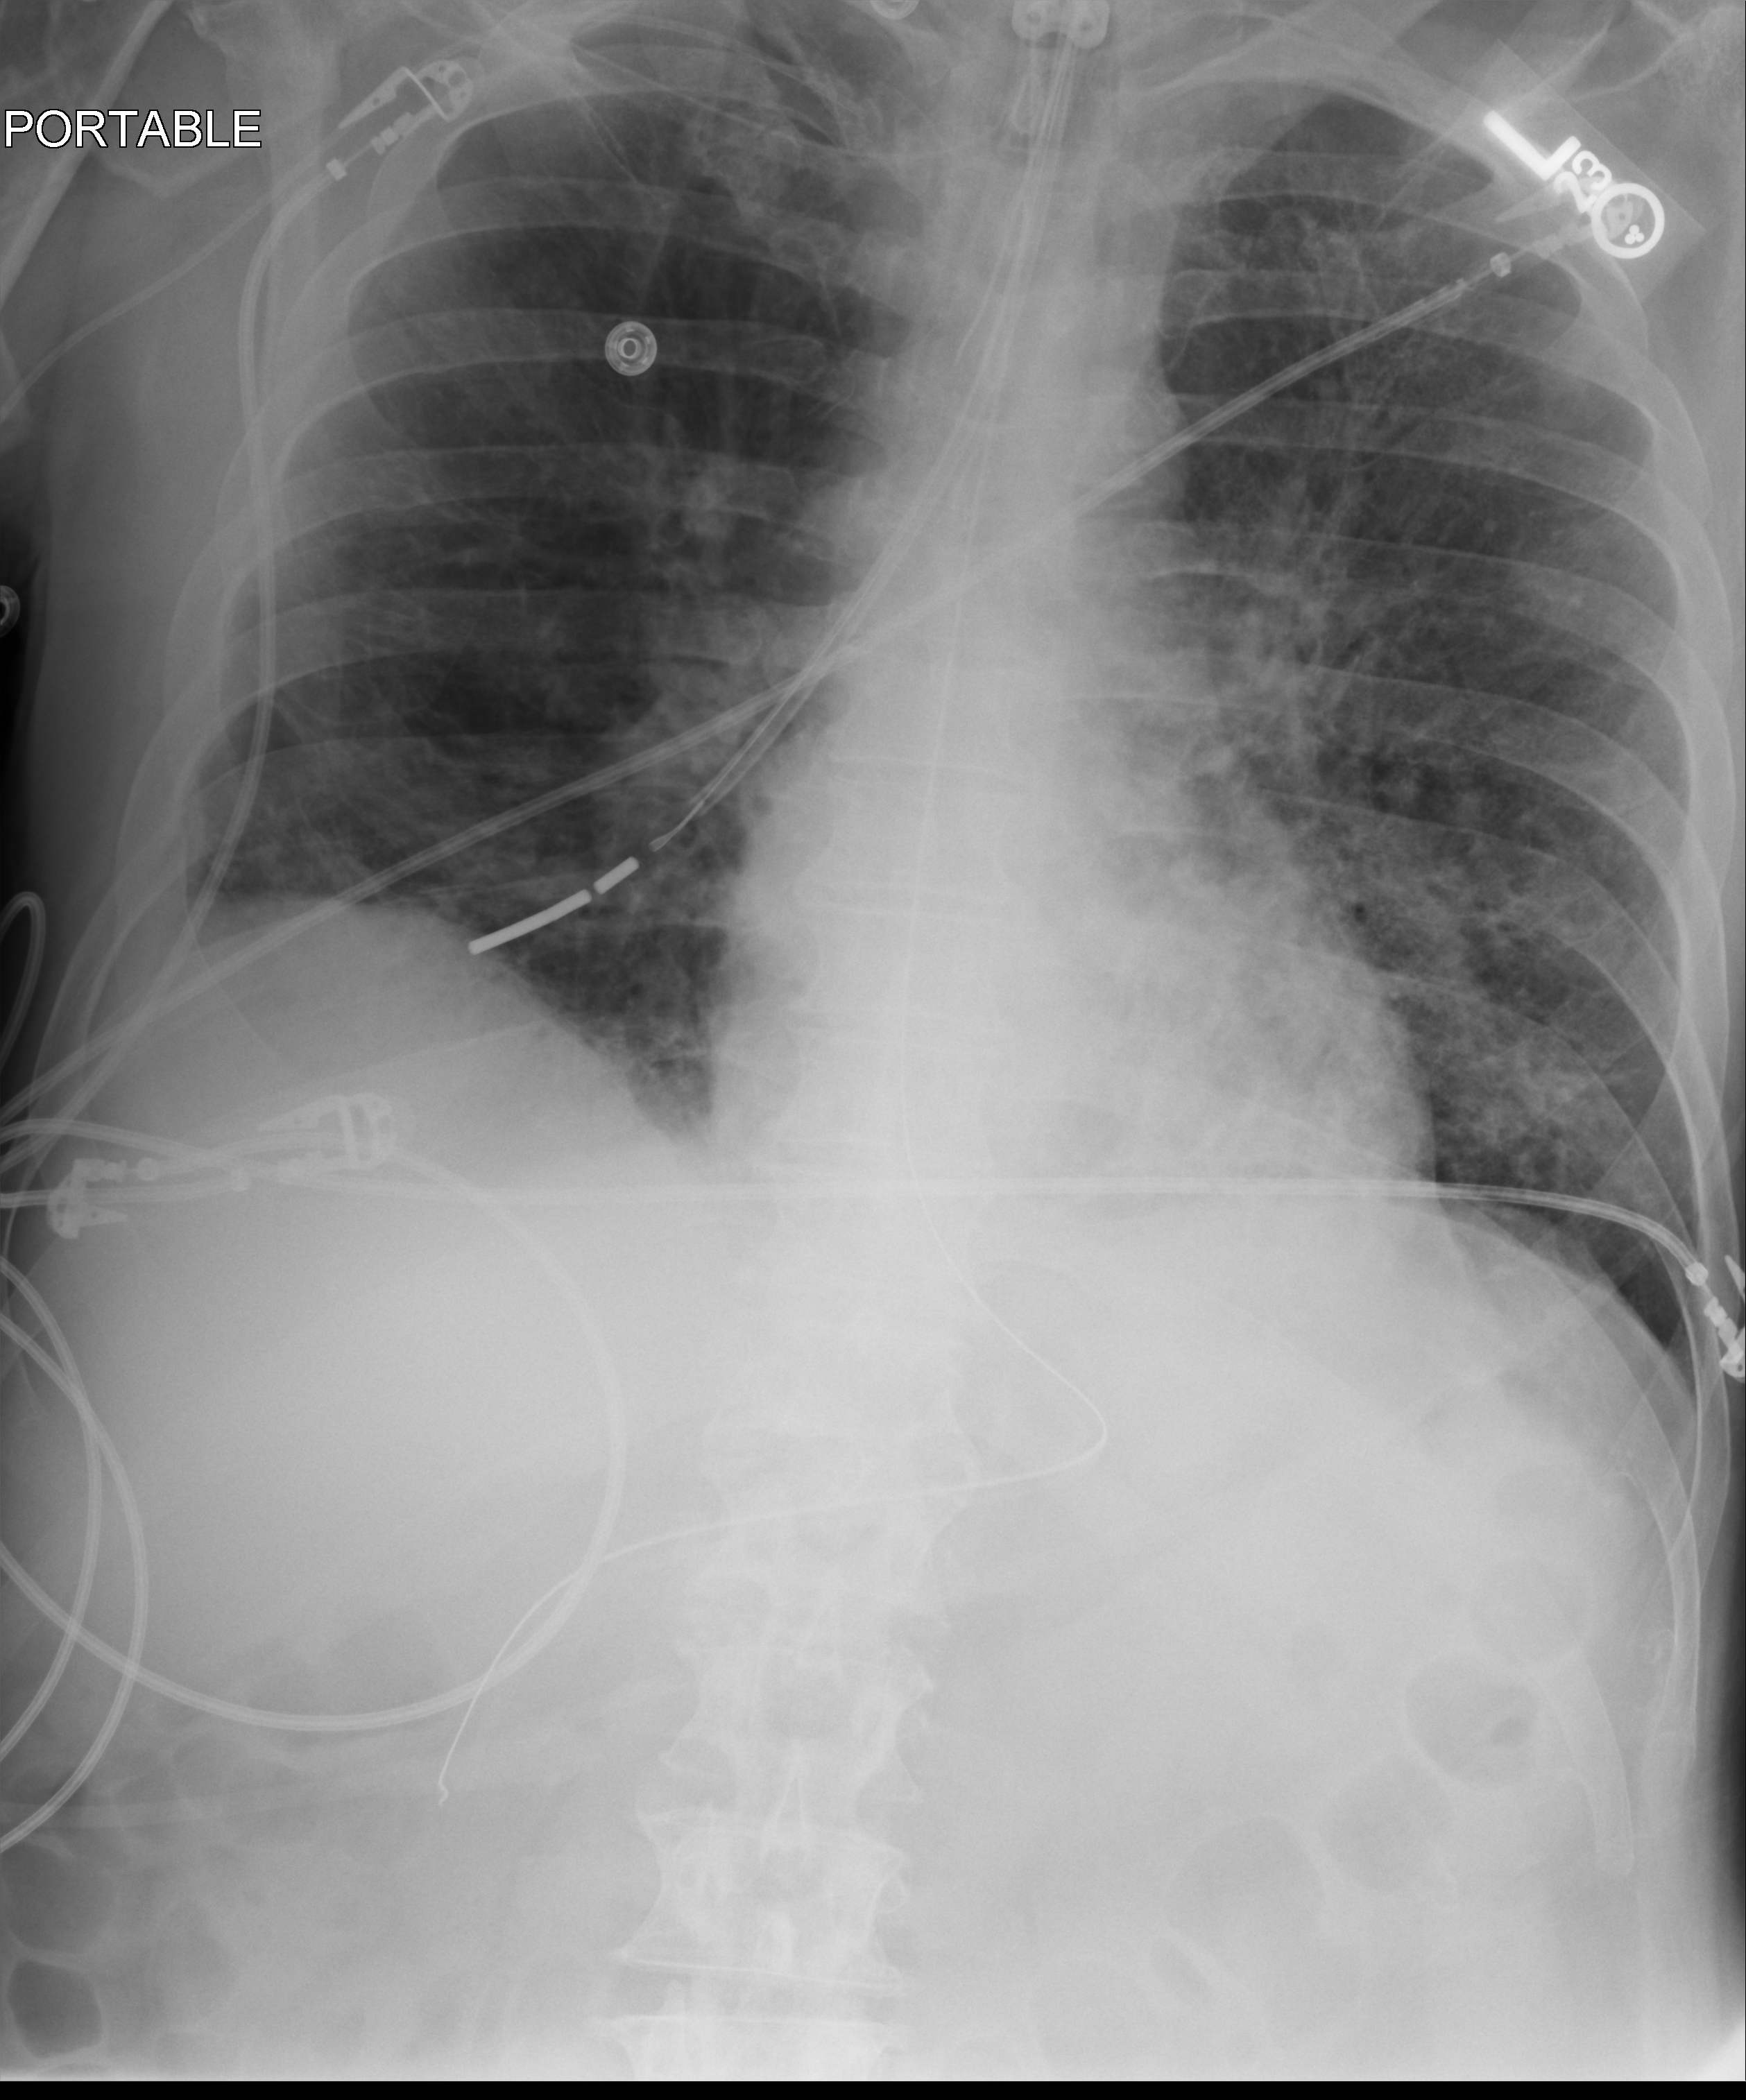
Chest X-ray (portable), anteroposterior (AP) projection. Male patient hospitalised with COVID-19, age 60–74 years.
Admission-level facts for this patient (not findings on this image; timing relative to this image not recorded): admitted to intensive care during this hospital stay: yes; mechanically ventilated during this hospital stay: yes.